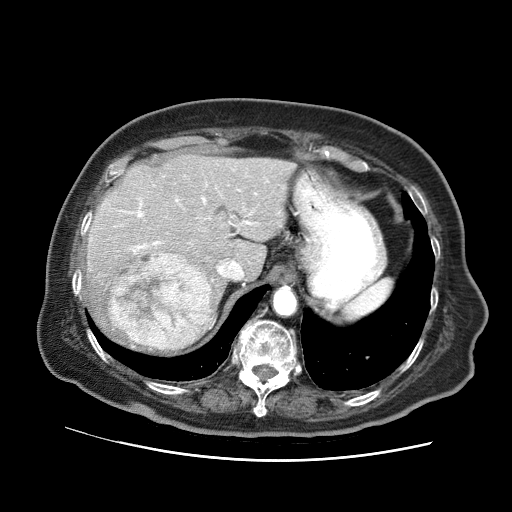
Contrast-enhanced abdominal CT (liver protocol), one axial slice; slice 50 of 73 in the series (ordered by position); 120 kVp; soft-tissue window (W 400 / L 40 HU); 2.5 mm slice thickness; 512 × 512 image matrix, field of view 380 × 380 mm. From the clinical record (not read from this slice): diagnosis: hepatocellular carcinoma (patient treated with transarterial chemoembolisation; whether this scan precedes or follows treatment is not stated here); TNM stage (as recorded): Stage-I; Child-Pugh class: A; tumour differentiation: well differentiated; tumour nodularity: uninodular.
Outlined on this slice (semi-automatically segmented with operator editing):
- liver parenchyma outside the tumour (the mass and vessels are separate outlines, so this box may not span the whole liver): bounding box (x1, y1, x2, y2) in pixels: (85, 154, 296, 354)
- mass: (104, 253, 212, 350)
- liver vessels: (119, 189, 256, 253)